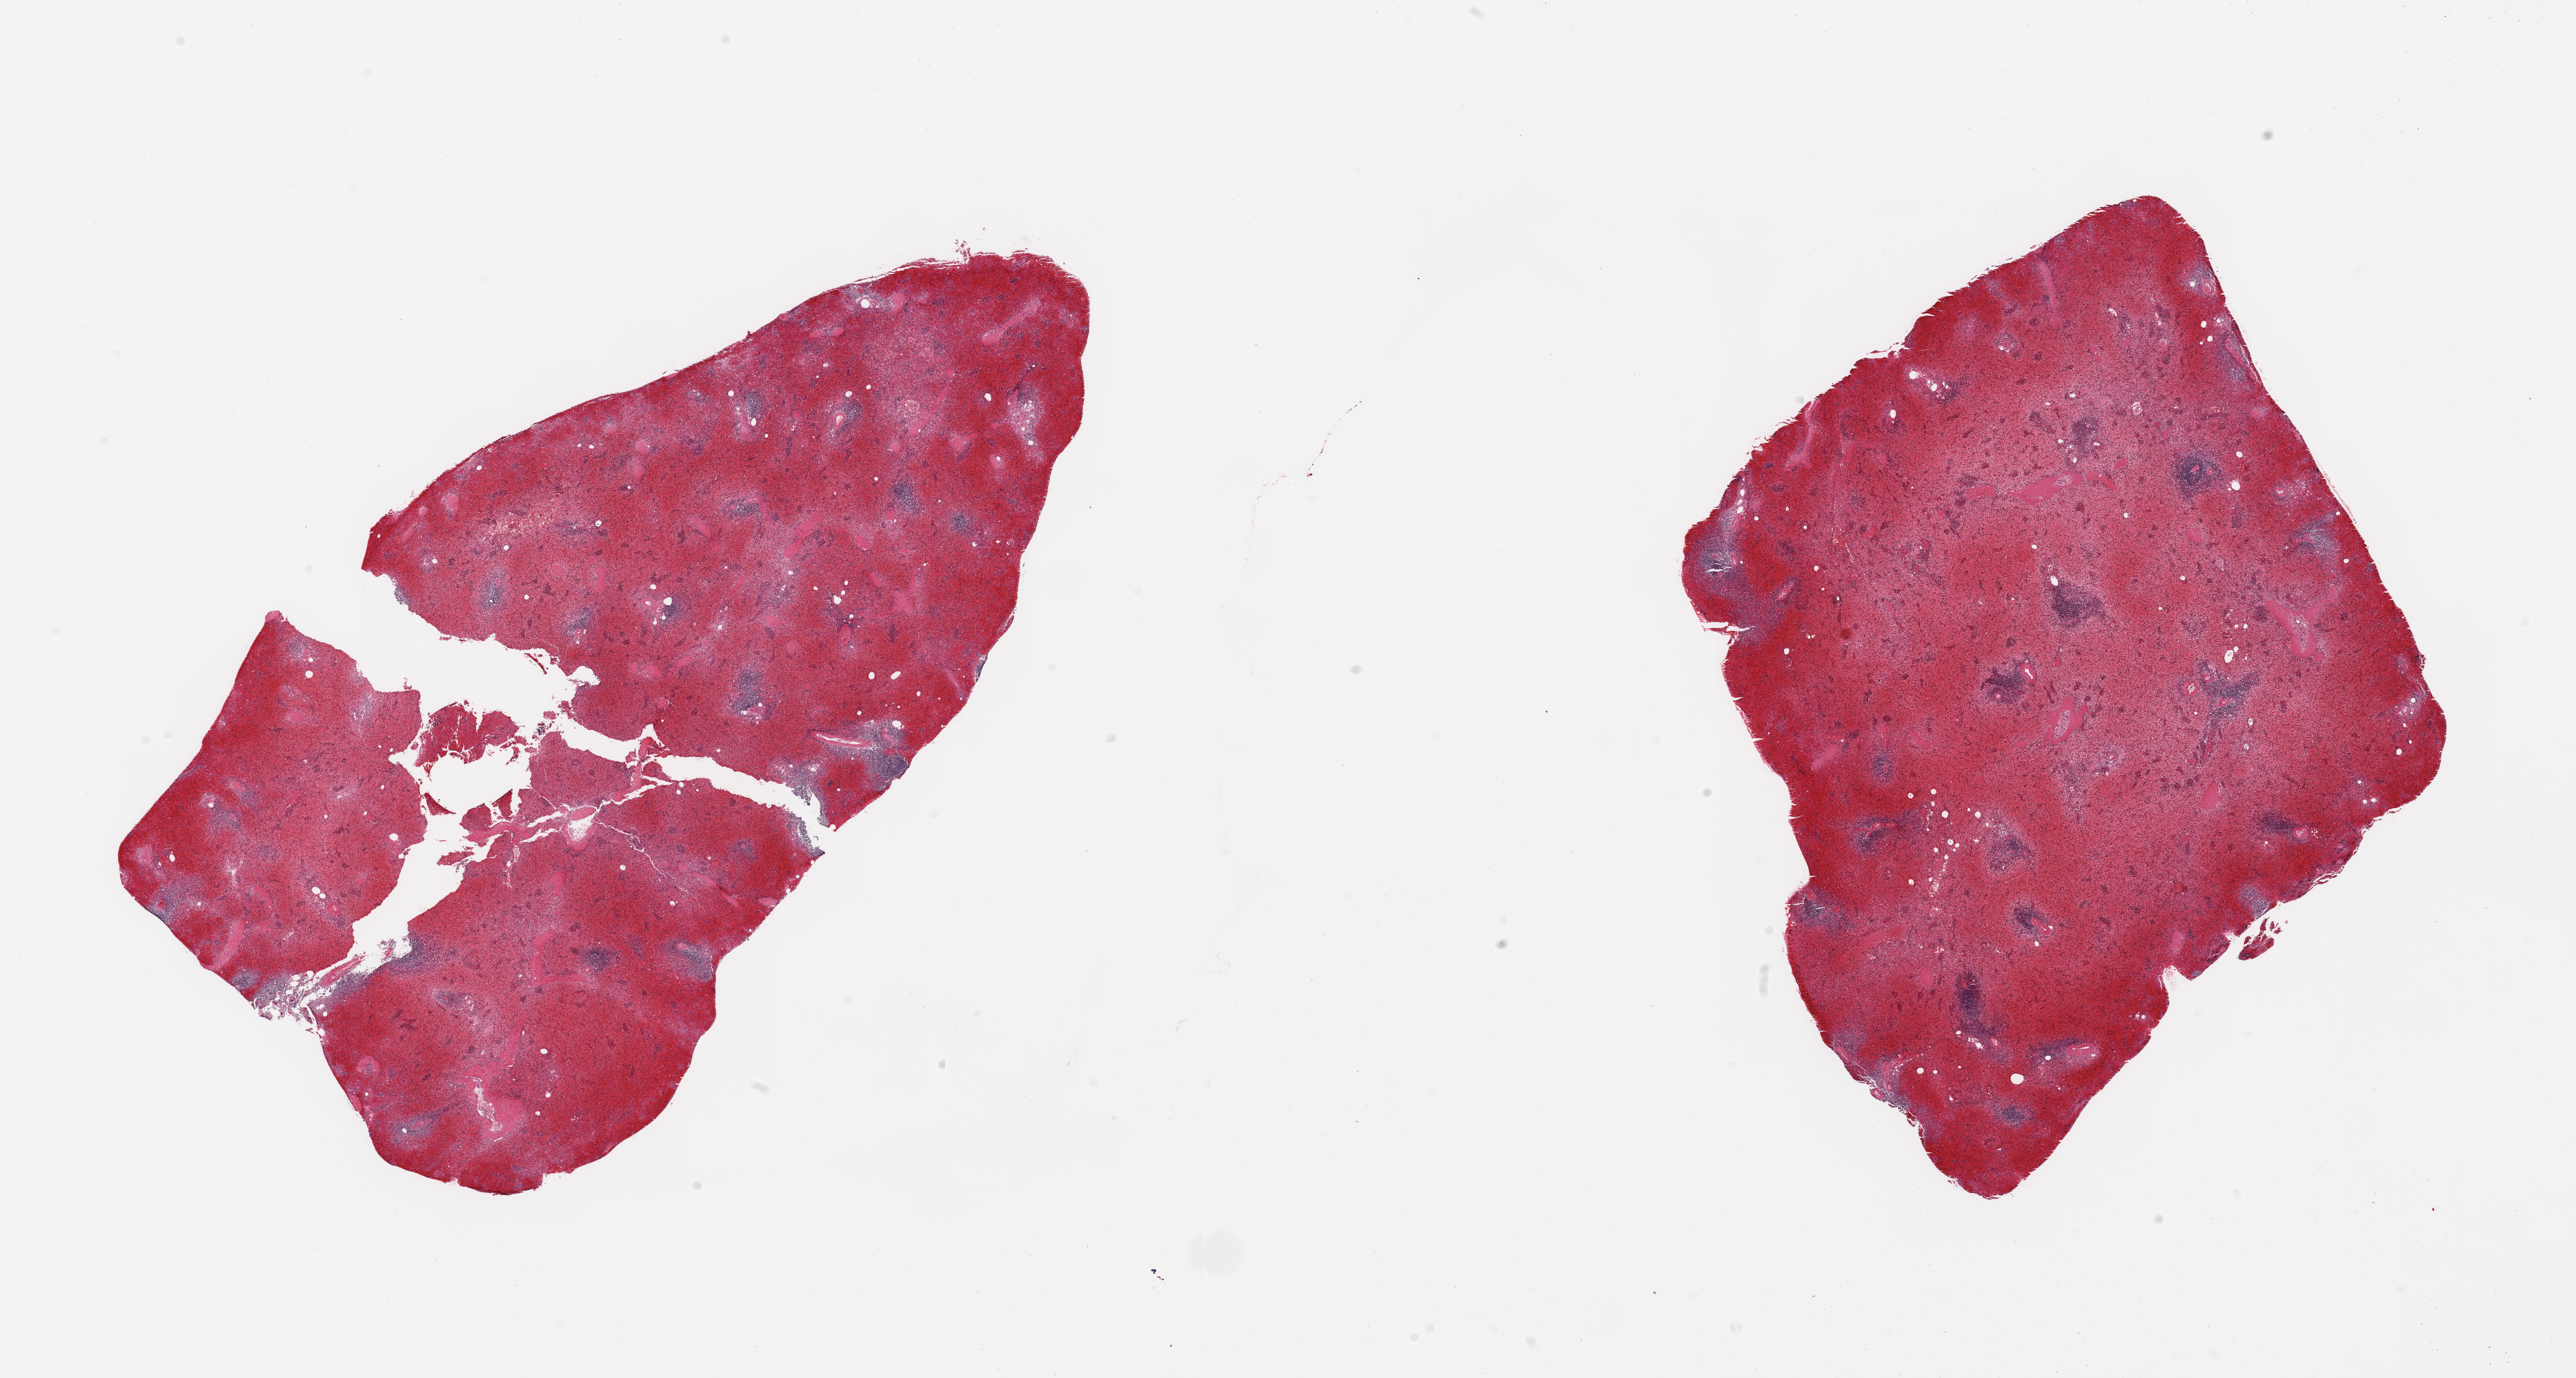
Haematoxylin and eosin whole-slide image, shown as a low-resolution overview of the whole scanned area (about 29.5 x 15.8 mm, from a 20x scan), PAXgene-fixed, paraffin-embedded tissue, target tissue: spleen, tissue donor sample. Donor: female.
• reviewer comment on this tissue sample: 2 pieces, marked congestion